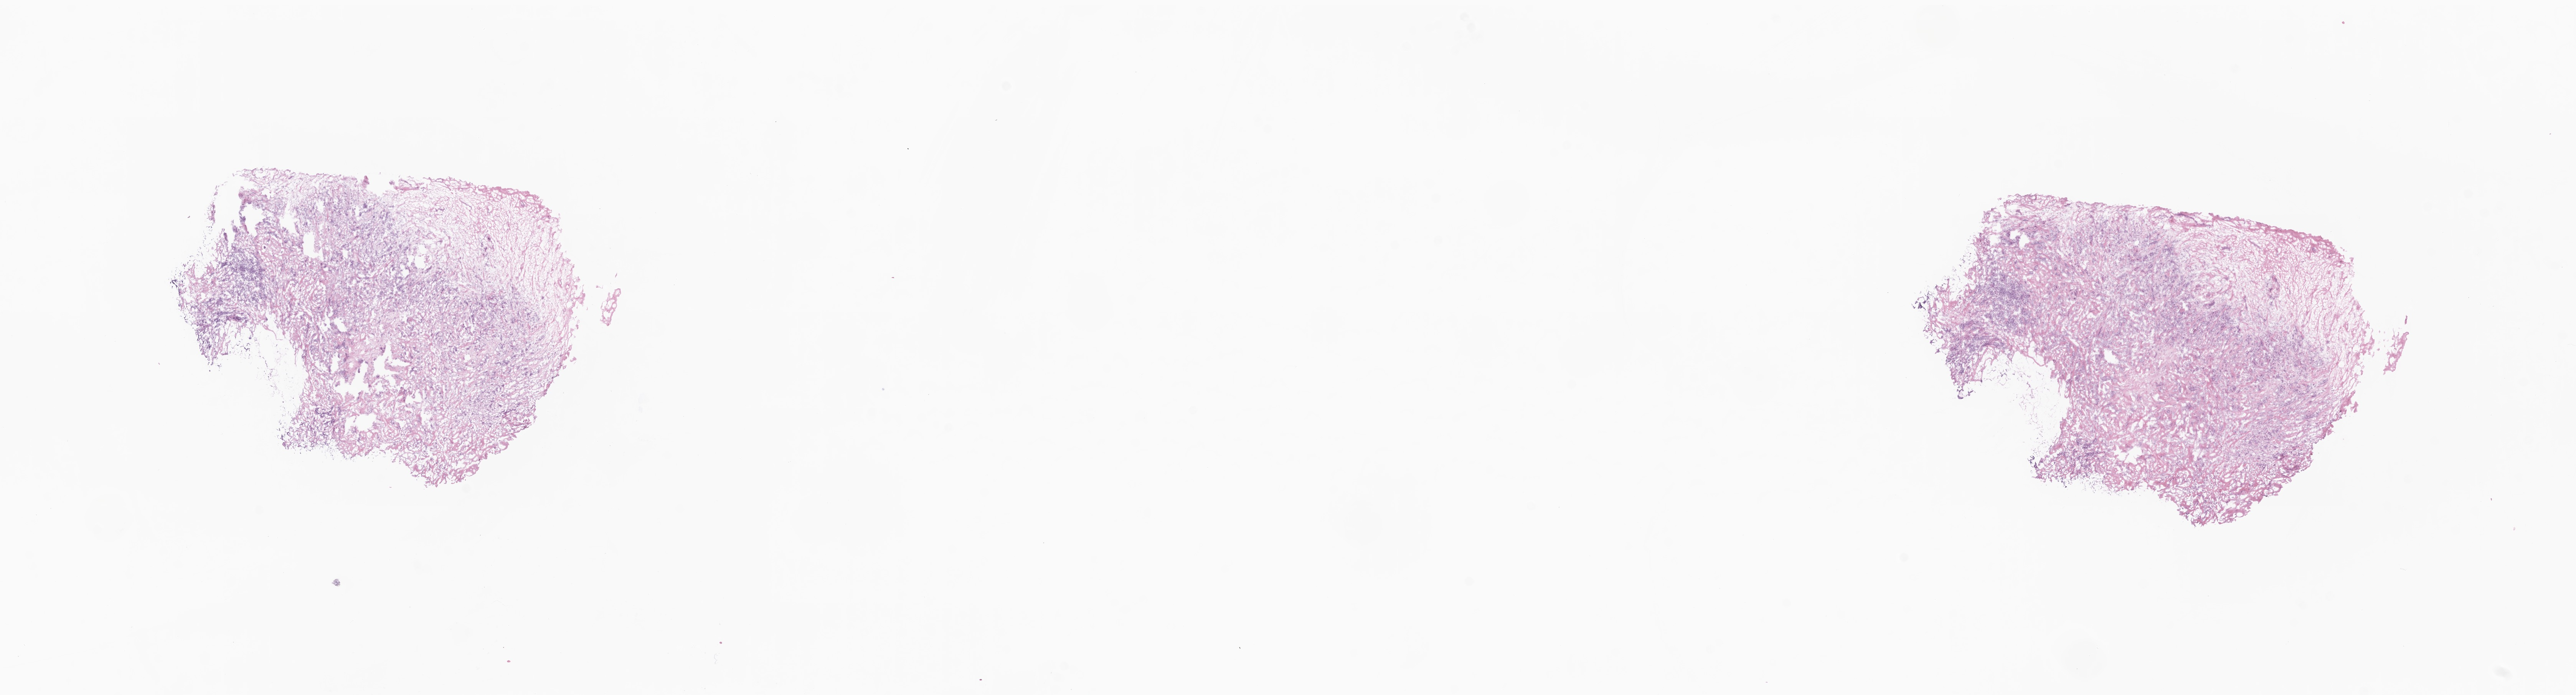
Whole-slide image, haematoxylin and eosin stain, a low-resolution overview of the entire scanned area, about 28.3 x 7.6 mm, frozen section (tissue freezing medium), primary tumor, anatomic site: breast. Female patient; age at initial diagnosis 81 years. Pathologist review of this section (percent, as recorded): tumor cells 75%, tumor nuclei 62%.
Diagnosis: Infiltrating duct carcinoma, NOS.